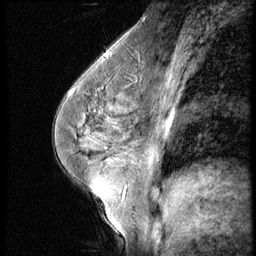
Breast MRI (dynamic contrast-enhanced), one sagittal slice. Position 28 of 56 along the scan axis. 3 images stored at this slice position (order not interpretable as contrast timing). 1.5 T. TE 4.2 ms, TR 9 ms. 2.5 mm slice thickness. 256 × 256 image matrix, field of view 180 × 180 mm. Female patient, age 45 years. Case-level facts recorded for this patient, not image findings: setting: breast cancer imaged before/during neoadjuvant chemotherapy; receptor status: HR-positive, HER2-negative.
Annotated regions visible in this slice (semi-automatically segmented with operator editing):
- analysis volume of interest (the breast-tissue region the enhancement analysis was run in; not a lesion): bounding box <102,77,166,129> (left, top, right, bottom; pixels)
- tumour enhancement mask (voxels above the 140 % enhancement threshold inside the analysis volume of interest): <102,80,128,124>